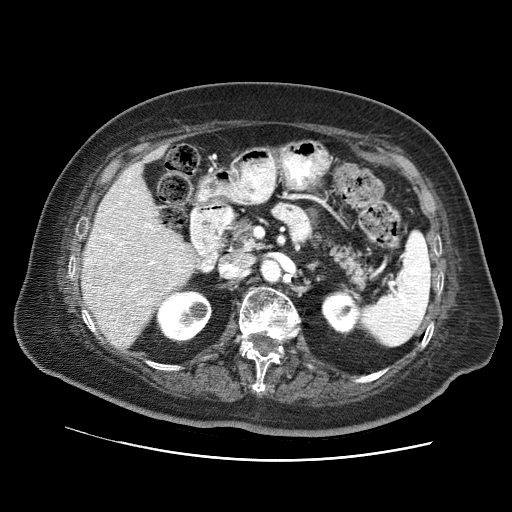
Contrast-enhanced abdominal CT (liver protocol), one axial slice; position 32 of 73 along the scan axis; 120 kVp; soft-tissue window (W 400 / L 40 HU); 2.5 mm slice thickness; 512 × 512 image matrix, field of view 380 × 380 mm. Case-level facts recorded for this patient, not image findings: diagnosis: hepatocellular carcinoma (patient treated with transarterial chemoembolisation; whether this scan precedes or follows treatment is not stated here); TNM stage (as recorded): Stage-I; Child-Pugh class: A; tumour nodularity: uninodular.
Outlined on this slice (semi-automatic segmentation, software-assisted and operator-edited):
- liver parenchyma outside the tumour (the mass and vessels are separate outlines, so this box may not span the whole liver): bounding box (x1, y1, x2, y2) in pixels: (82, 148, 197, 348)
- liver vessels: (87, 180, 171, 318)